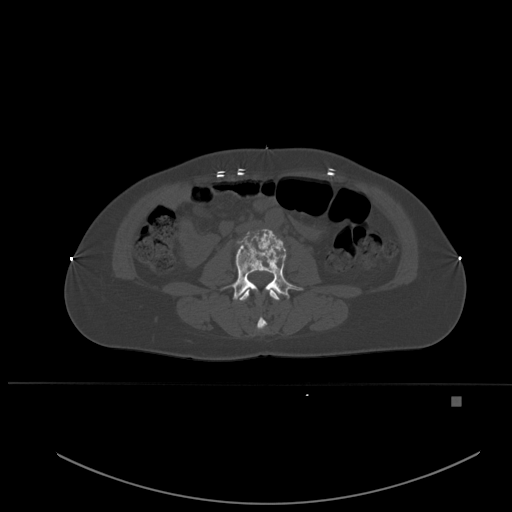
CT including the spine, one axial slice. Bone window (W 1800 / L 400 HU). 1.5 mm slice thickness. 512 × 512 image matrix, field of view 443 × 443 mm. Patient: female, 49 years. Case-level facts recorded for this patient, not image findings: primary cancer: breast.
Outlined on this slice (semi-automatic segmentation, software-assisted and operator-edited):
- L2 vertebra: box from (x=239, y=289) to (x=280, y=329) px
- L3 vertebra: (x=223, y=231)–(x=303, y=300)